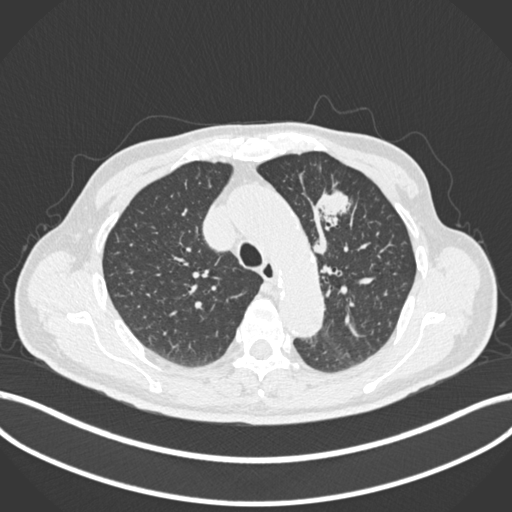
Chest CT, one axial slice. Slice 182 of 261 in the series (ordered by position). Reconstruction kernel B30f. Lung window (W 1500 / L -600 HU). 1 mm slice thickness. 512 × 512 image matrix. Male patient, age 74 years. Case-level facts recorded for this patient, not image findings: clinical TNM (as recorded): T2b N0 M1c.
Annotated regions visible in this slice (bounding box drawn by a radiologist):
- lung tumour (recorded histology: adenocarcinoma): bounding box [x1, y1, x2, y2] px = [305, 182, 358, 236]